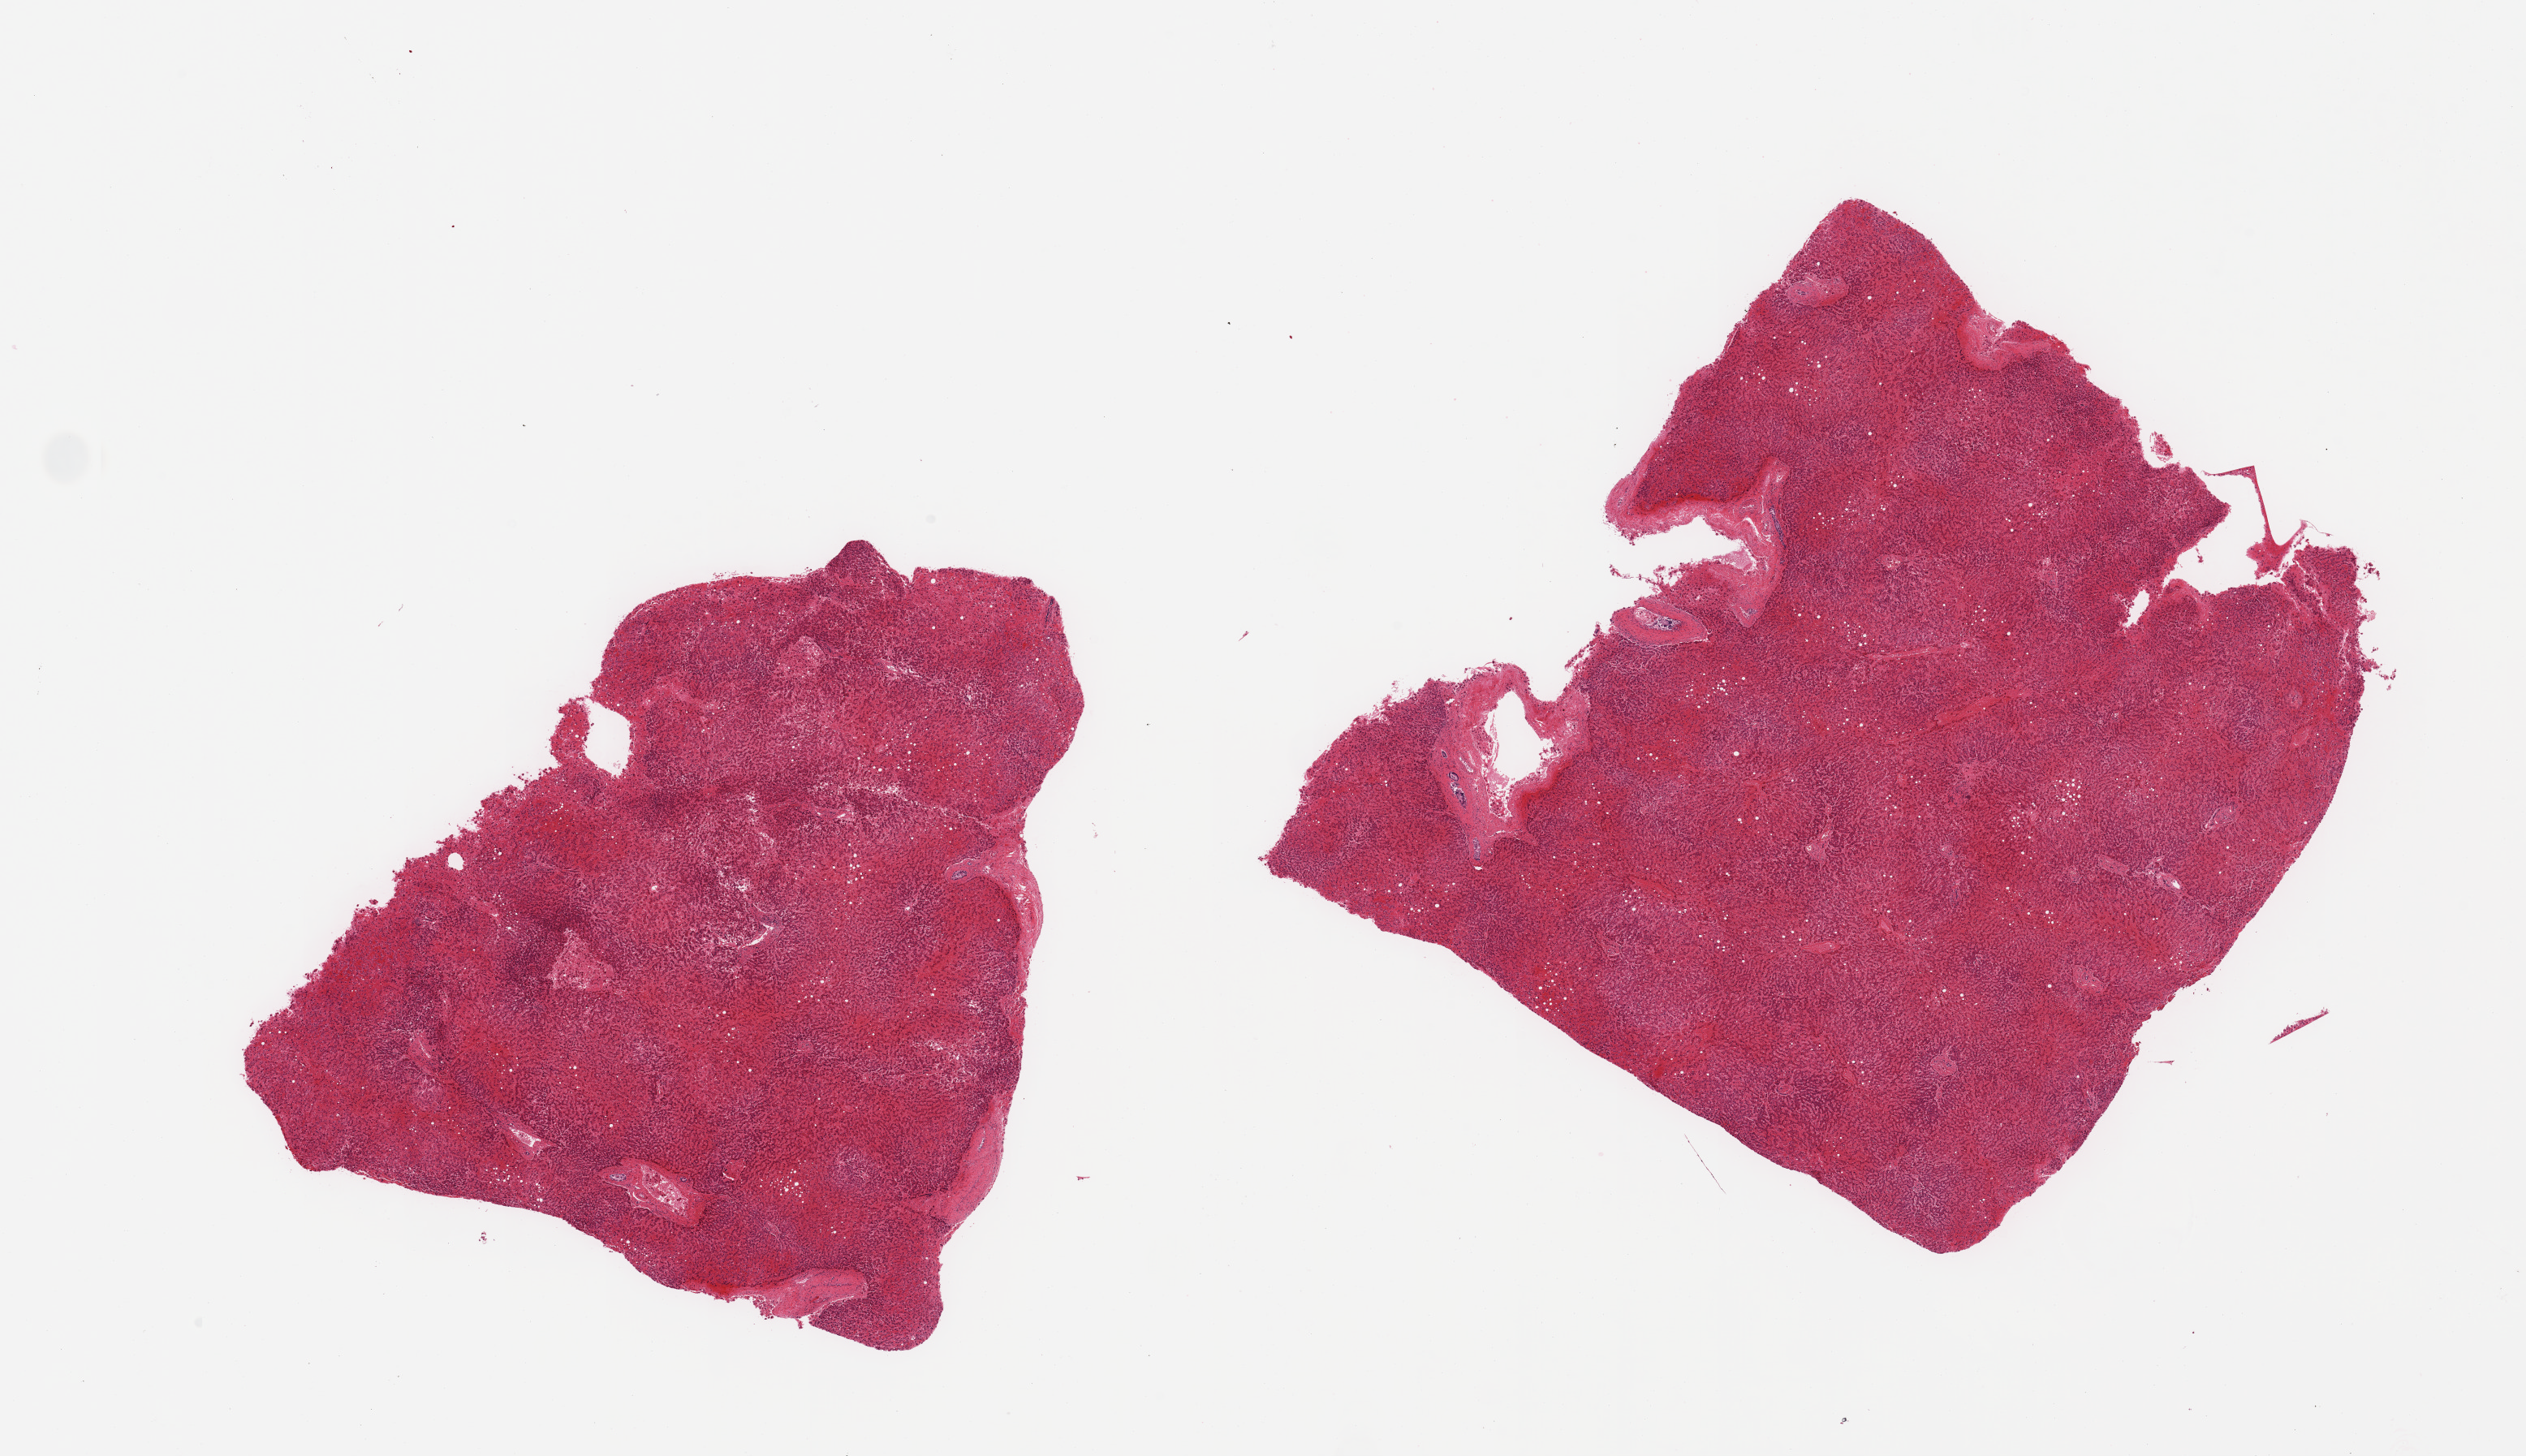
Whole-slide image, H&E stain, brightfield, a low-resolution overview of the entire scanned area, about 24.6 x 14.2 mm (acquisition: 20x scan); PAXgene-fixed paraffin-embedded (PFPE) section; target tissue: liver; tissue donor sample.
Review note (as recorded): 2 pieces, marked passive congestion, focal areas with early infarction.